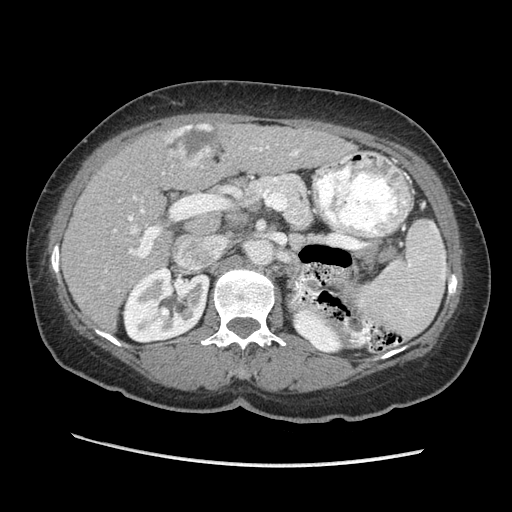
Contrast-enhanced abdominal CT (liver protocol), one axial slice; position 124 of 170 along the scan axis; reconstruction kernel STANDARD; soft-tissue window (W 400 / L 40 HU); 2.5 mm slice thickness; 512 × 512 image matrix, field of view 360 × 360 mm. From the clinical record (not read from this slice): diagnosis: hepatocellular carcinoma (patient treated with transarterial chemoembolisation; whether this scan precedes or follows treatment is not stated here); TNM stage (as recorded): Stage-II; Child-Pugh class: A; tumour nodularity: multinodular; tumour size: 4 cm.
Structures marked on this image (semi-automatically segmented with operator editing):
- liver parenchyma outside the tumour (the mass and vessels are separate outlines, so this box may not span the whole liver): bounding box (x1, y1, x2, y2) in pixels: (62, 122, 355, 328)
- mass: (166, 125, 220, 167)
- liver vessels: (114, 146, 350, 258)